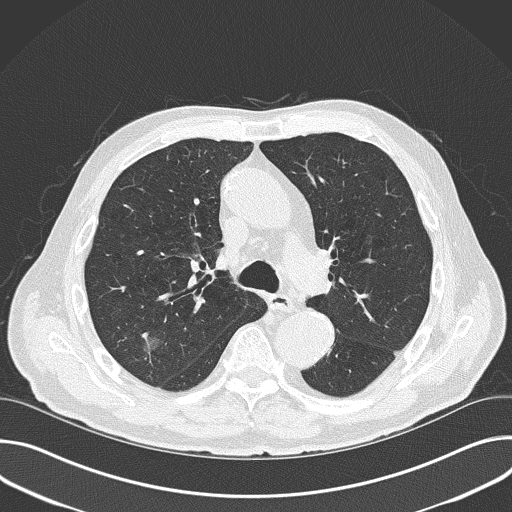
Axial slice from a low-dose chest CT screening exam, baseline screening round, lung window (W 1500 / L -600 HU), lung (sharp) reconstruction kernel (B50f), slice 108 of 177 in the series. Male, age 74 years at enrolment.
• Expert-annotated lung lesion, bounding box (x1, y1, x2, y2) in pixels: (126, 321, 174, 368).
• The screening reader recorded 3 non-calcified nodules or masses ≥4 mm on this exam (right upper lobe, right upper lobe, right middle lobe); which of them this box marks is not recorded.
• Official screen result: positive, change unspecified: nodule(s) >= 4 mm or enlarging nodule(s), mass(es), or other non-specific abnormalities suspicious for lung cancer.
• Later outcome: lung cancer diagnosed 215 days after this screen — small cell carcinoma, NOS, right upper lobe, stage IV (AJCC 6th edition), 15 mm at pathology.